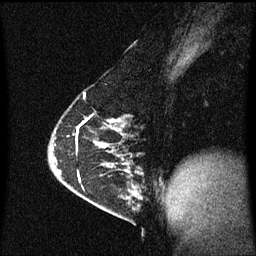
Breast MRI (dynamic contrast-enhanced), one sagittal slice. Dynamic contrast-enhanced series, image 2 of 3 at this slice position (ordered by acquisition). 1.5 T. TE 4.2 ms, TR 8.4 ms. 2 mm slice thickness. 256 × 256 image matrix, field of view 200 × 200 mm. Female patient, age 63 years.
Structures marked on this image (semi-automatic segmentation, software-assisted and operator-edited):
- analysis volume of interest (the breast-tissue region the enhancement analysis was run in; not a lesion): bounding box <98,170,143,217> (left, top, right, bottom; pixels)
- tumour enhancement mask (voxels above the 70 % enhancement threshold inside the analysis volume of interest): <126,170,139,197>